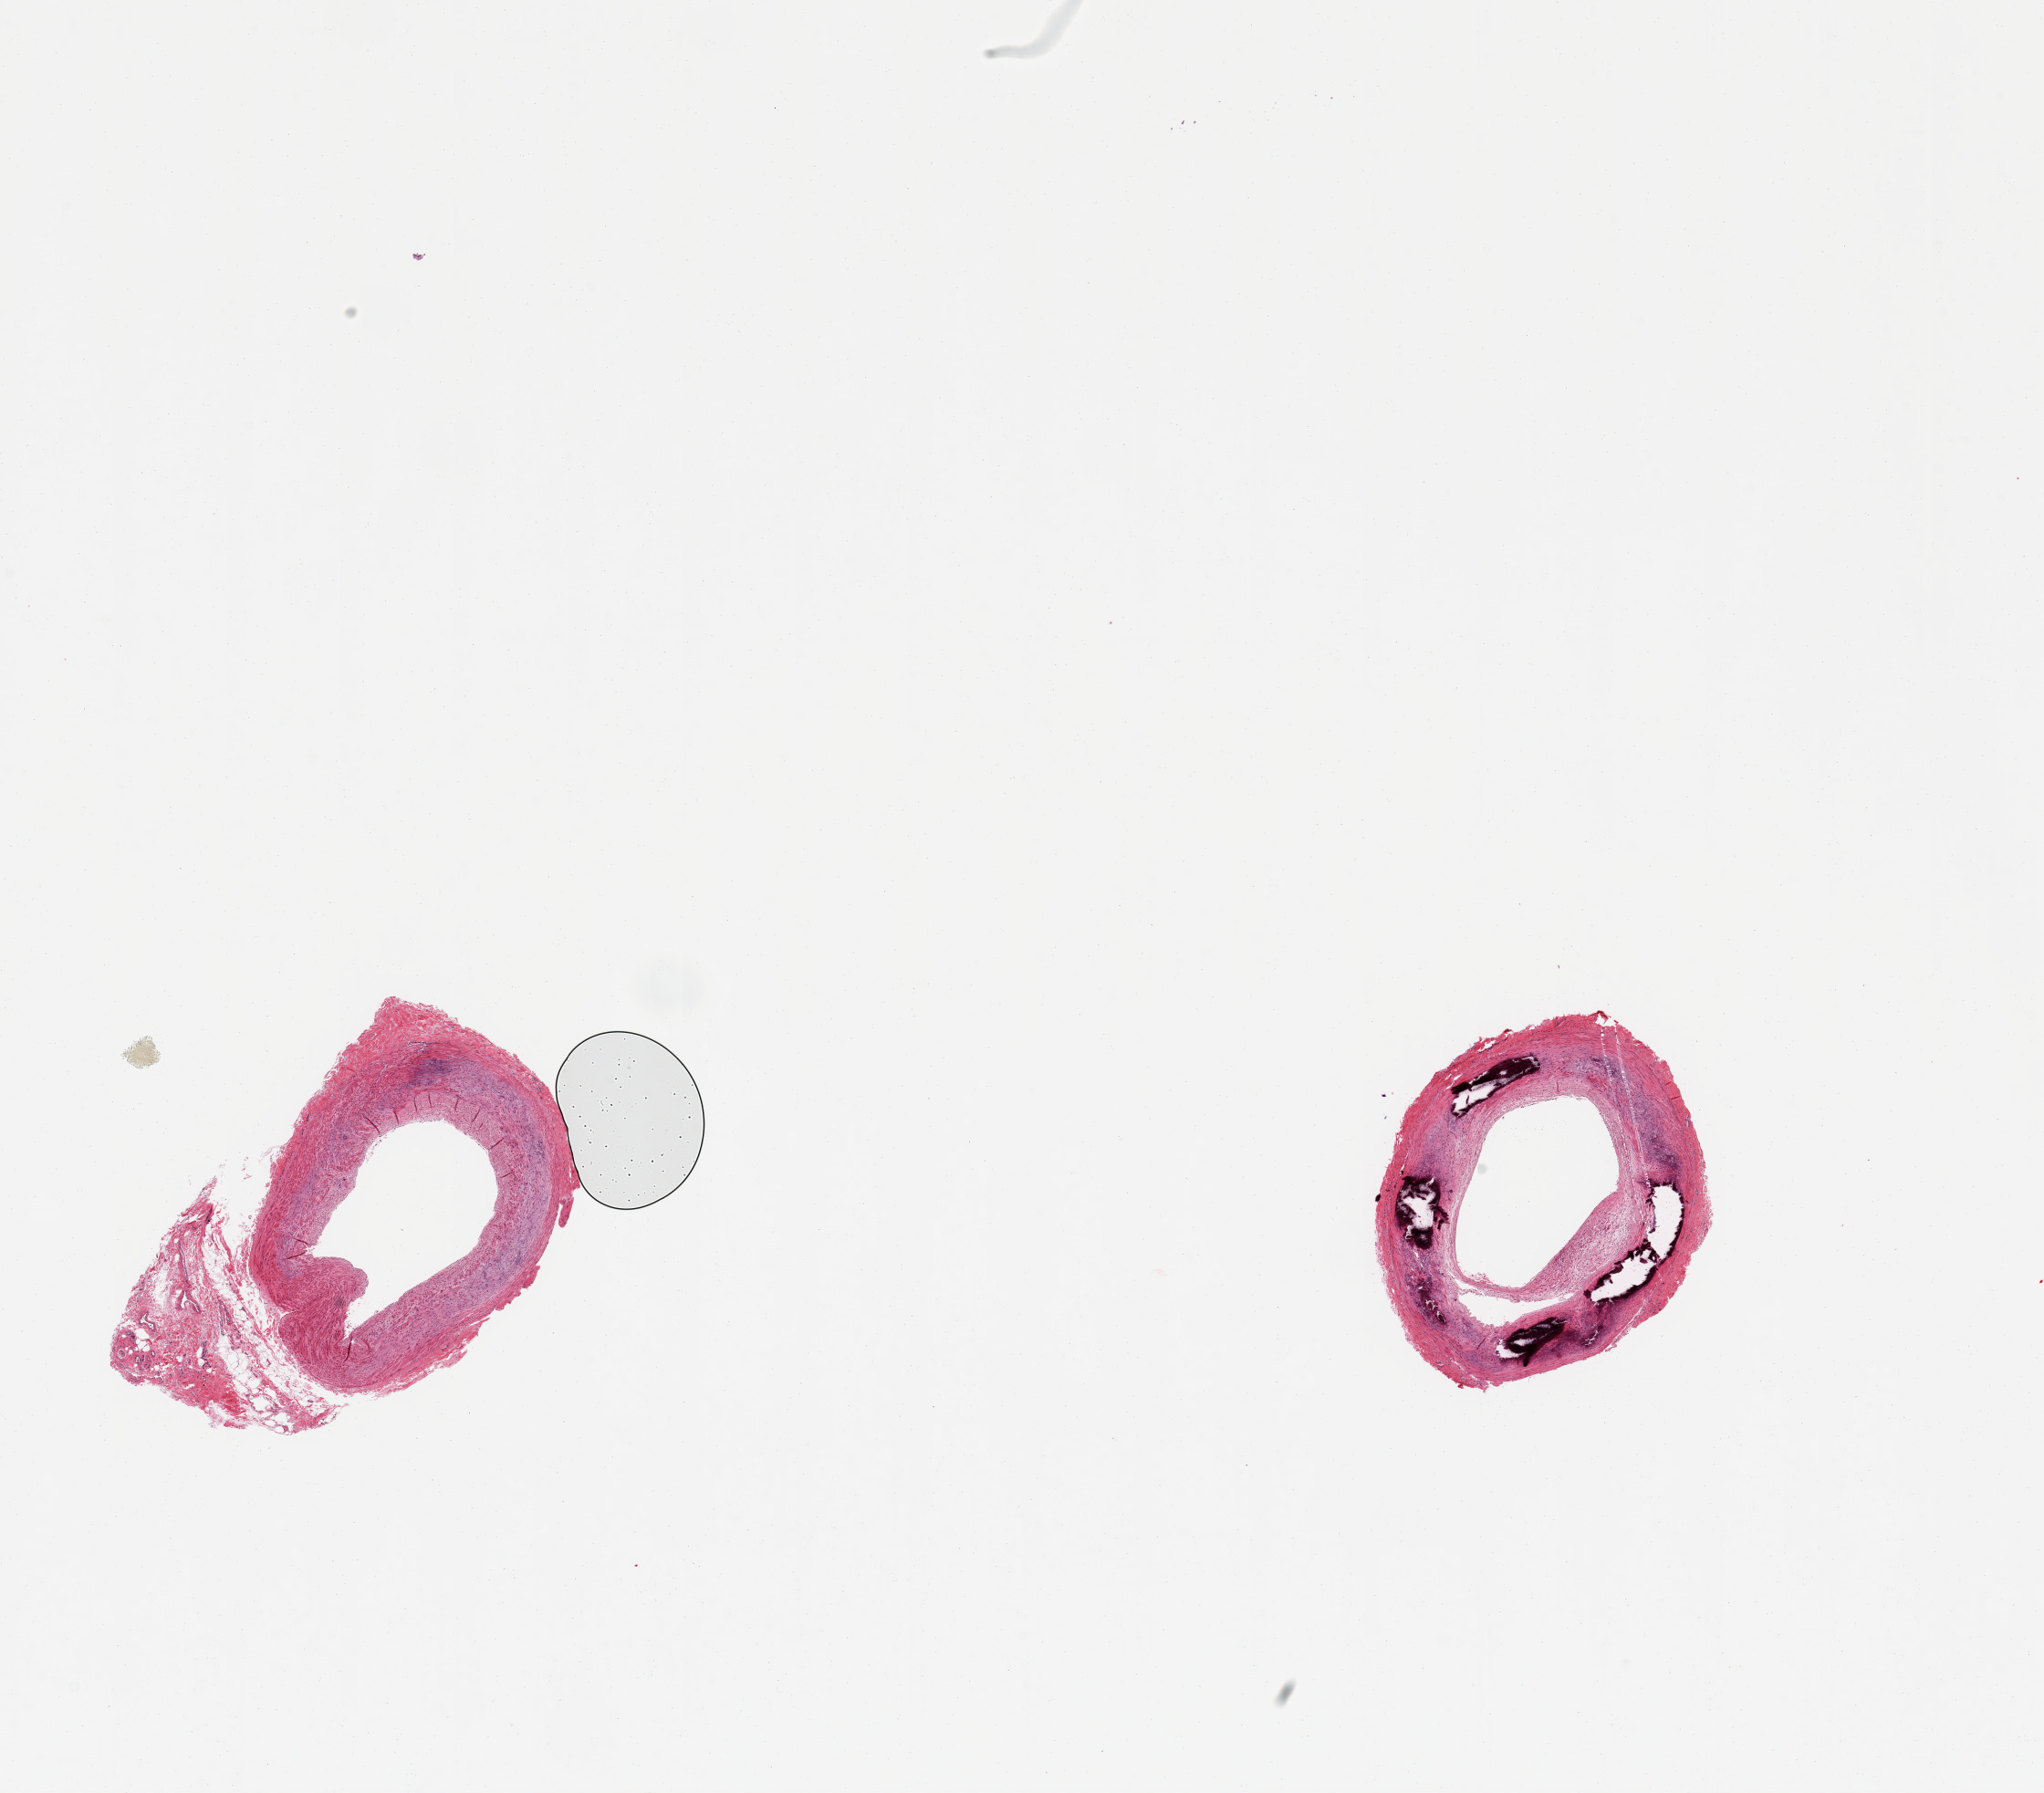
Whole-slide image, hematoxylin and eosin (H&E) stain — whole scanned area (about 17.7 x 15.5 mm) shown as a low-resolution overview. PAXgene-fixed, paraffin-embedded tissue. Sampled site (target tissue): tibial artery. Tissue donor sample. Donor: male.
Reviewer comment on this tissue sample: 2 pieces; one shows numerous medial calcifications and fibrosclerotic plaque; other with attached up to 1.4mm fibrofatty stroma.